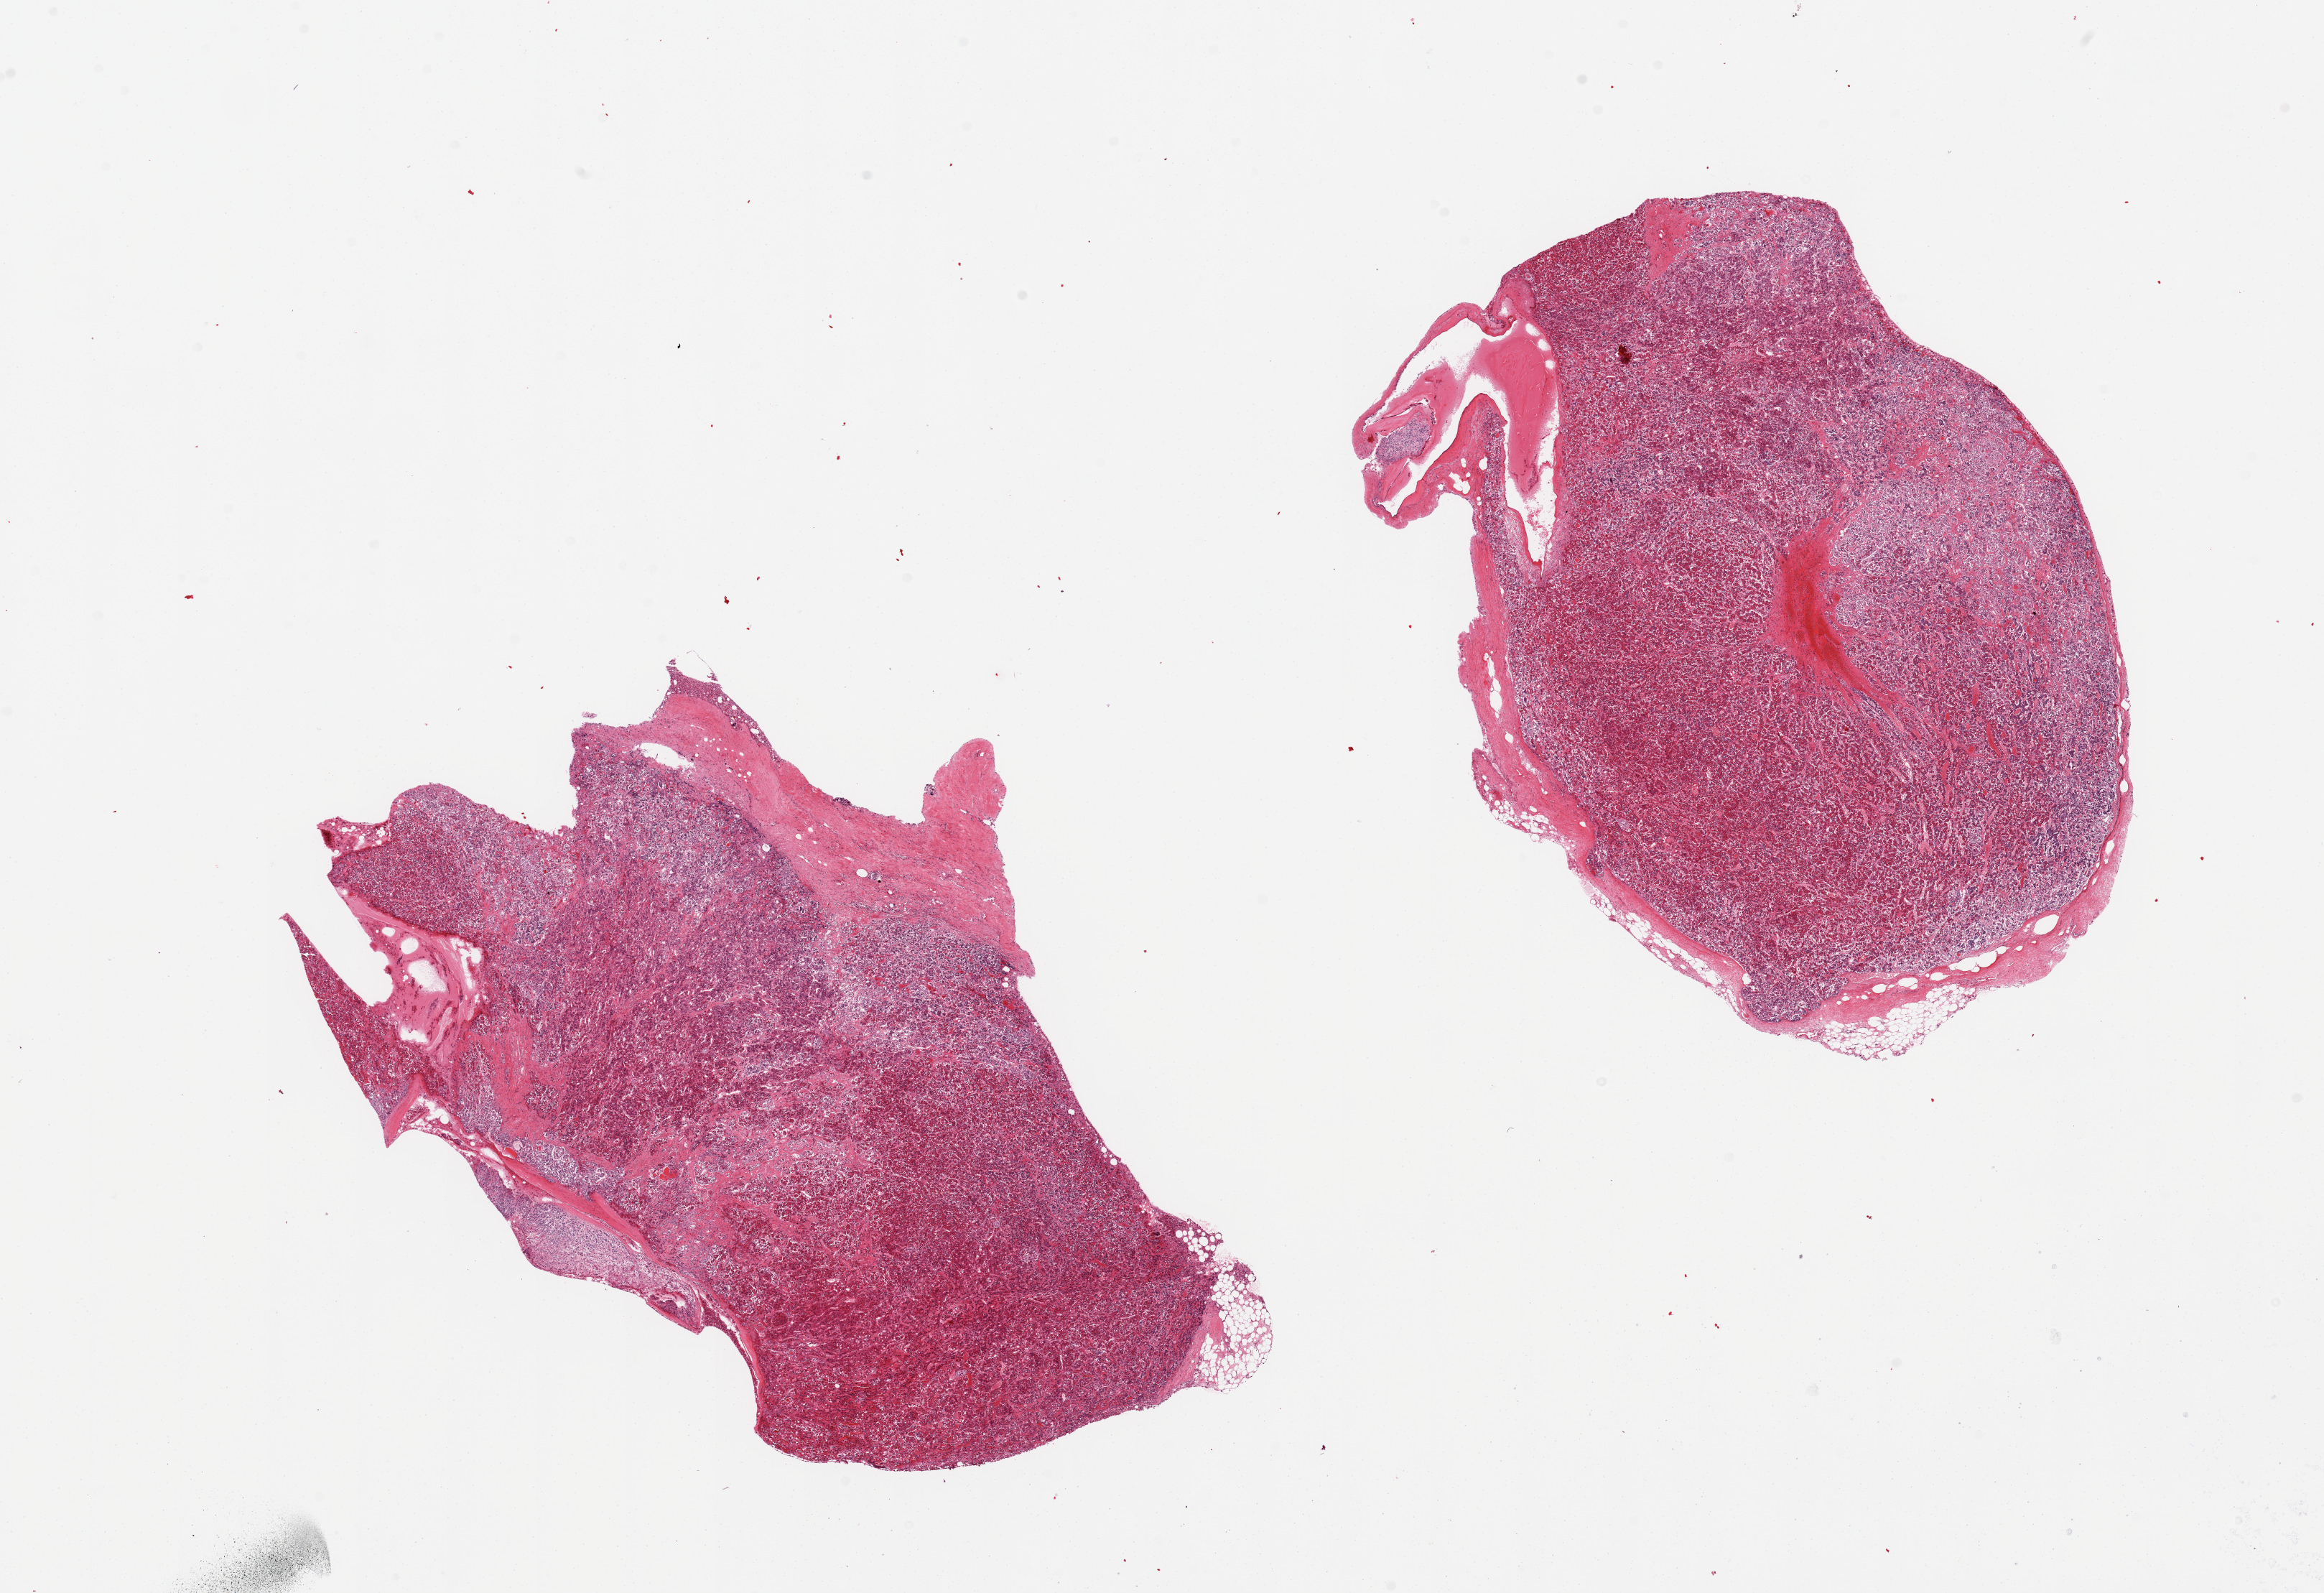
Whole-slide image, H&E stain — a low-resolution overview of the entire scanned area, about 25.6 x 17.5 mm; PAXgene-fixed paraffin-embedded (PFPE) section; target tissue: pituitary; donor tissue sample. Donor: male.
Reviewer comment on this tissue sample: 2 pieces, autolyzing adenohypophysis.